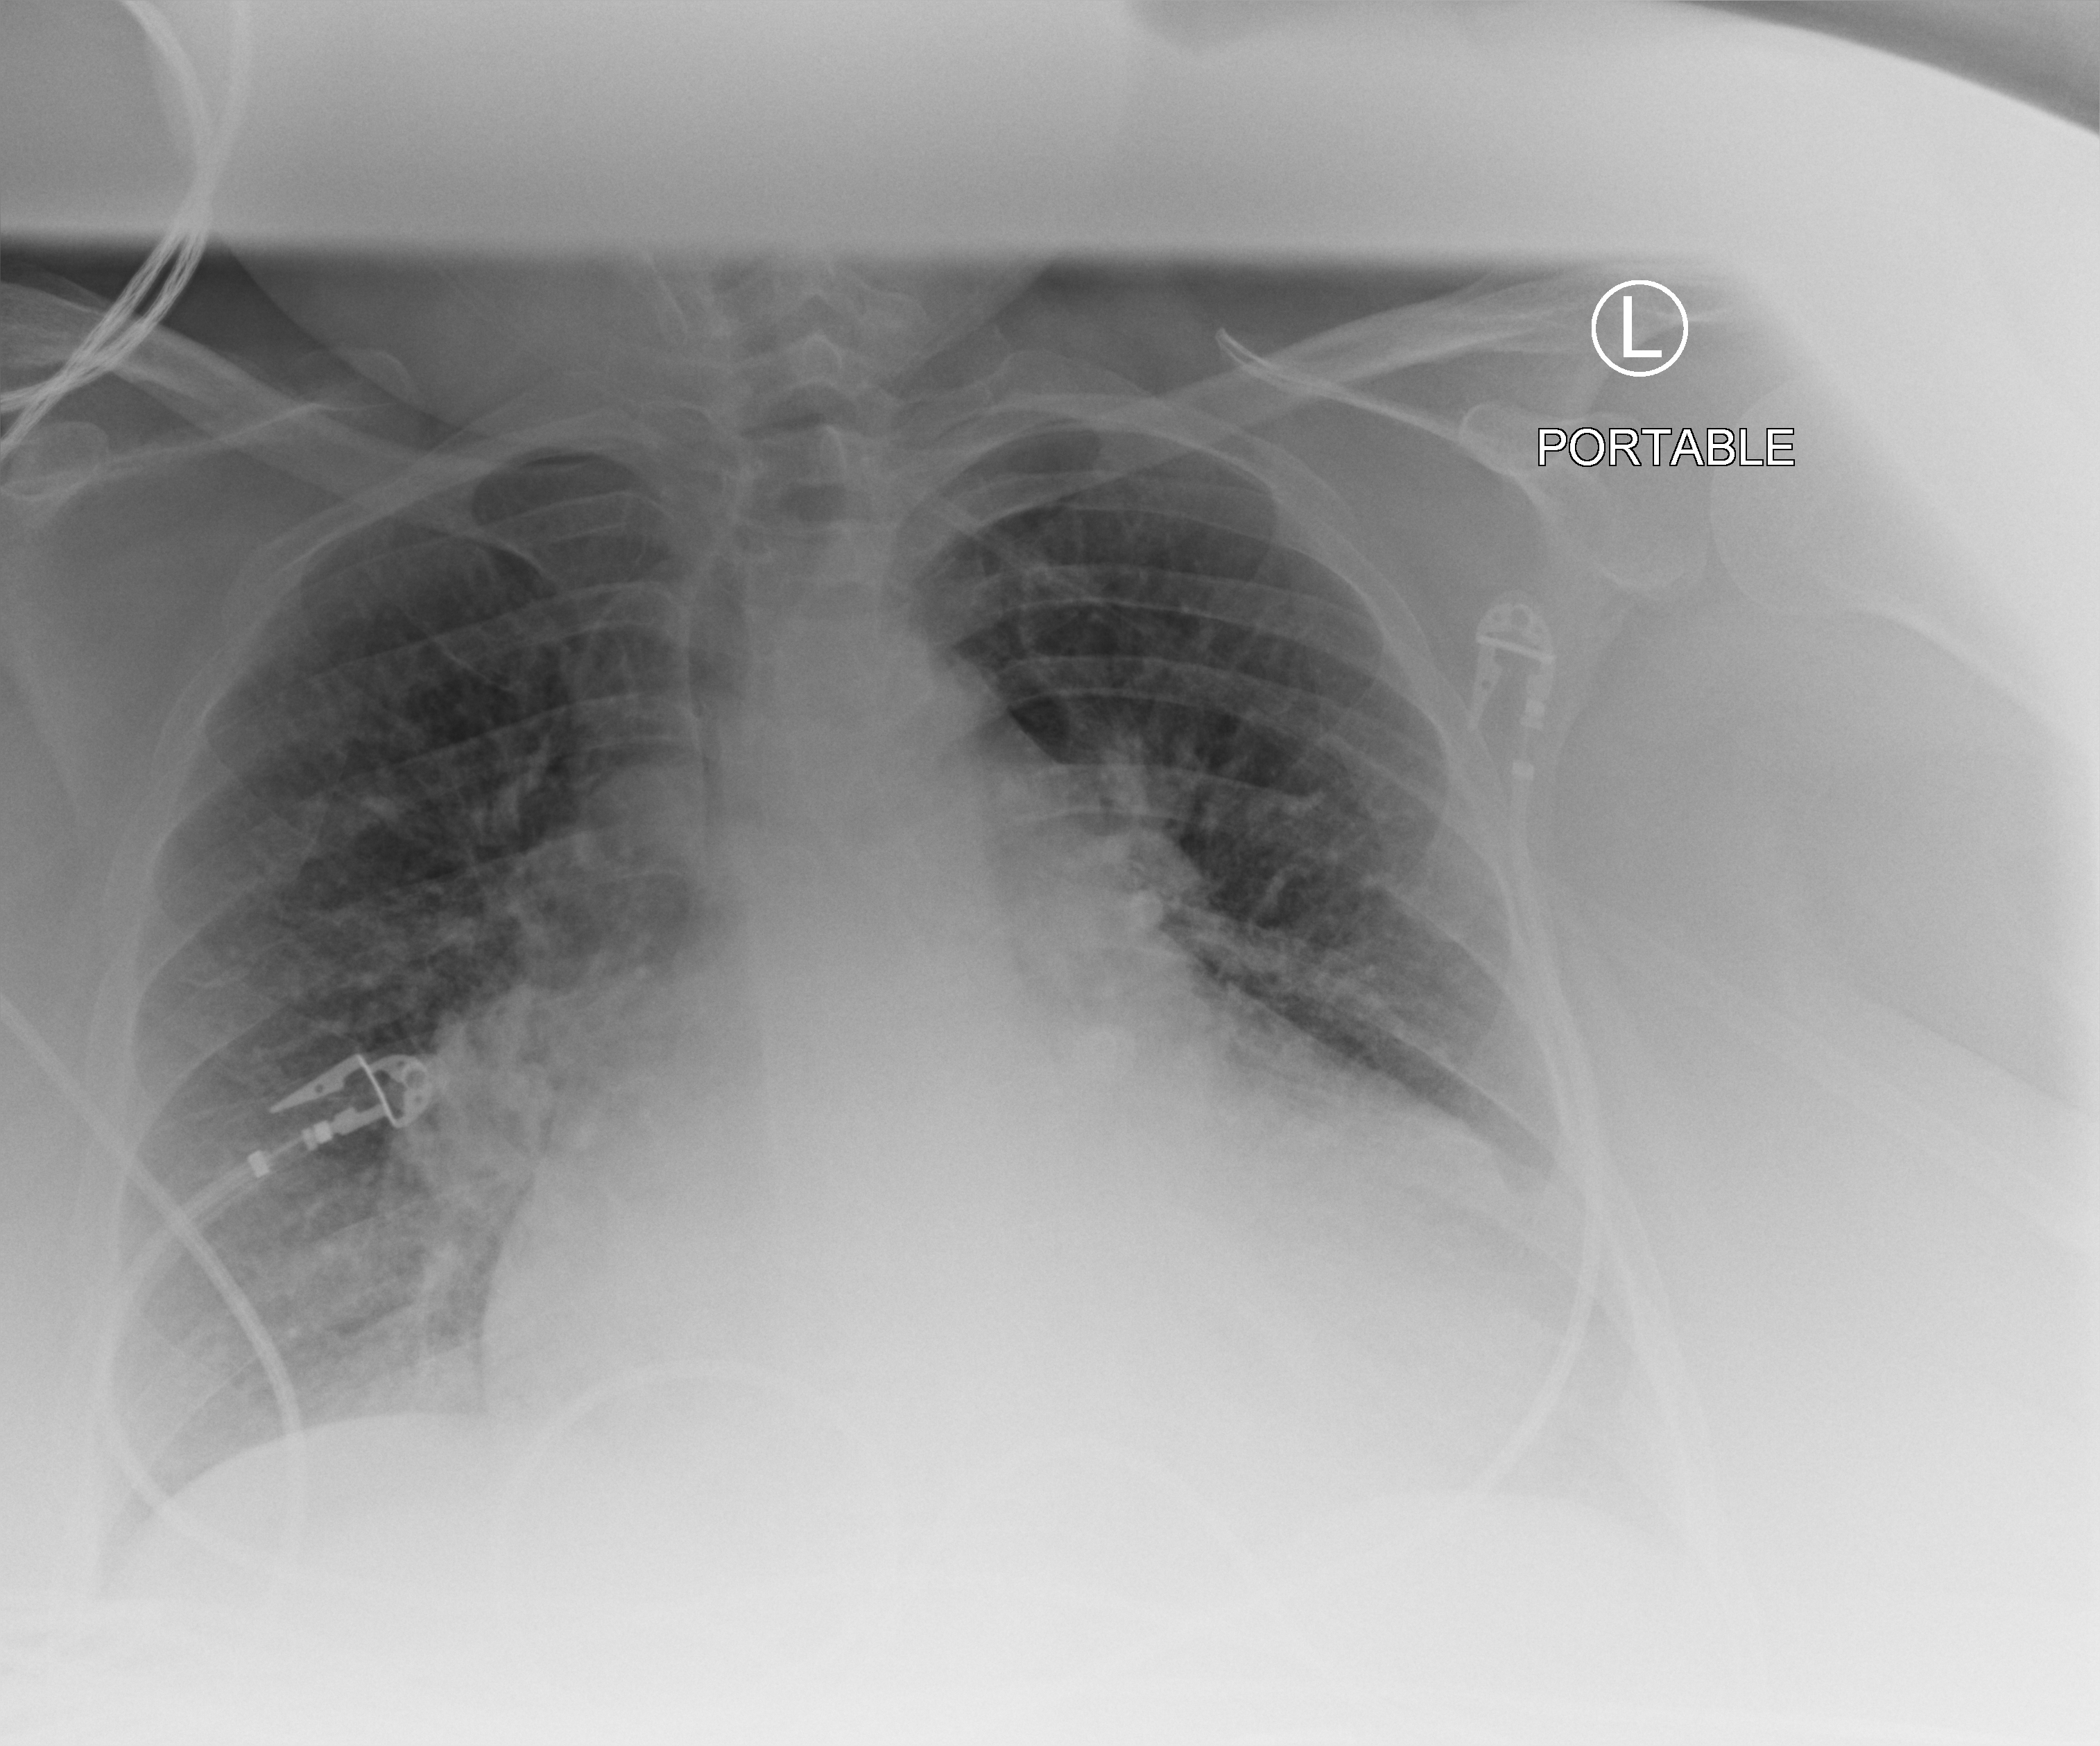
Bedside chest radiograph (computed radiography); anteroposterior (AP) projection. Patient hospitalised with COVID-19; female, aged 60–74 years.
From the hospital-stay record, not from the radiograph (when in the stay this image was taken is not recorded):
- admitted to intensive care during this hospital stay: yes
- length of hospital stay: 6 days